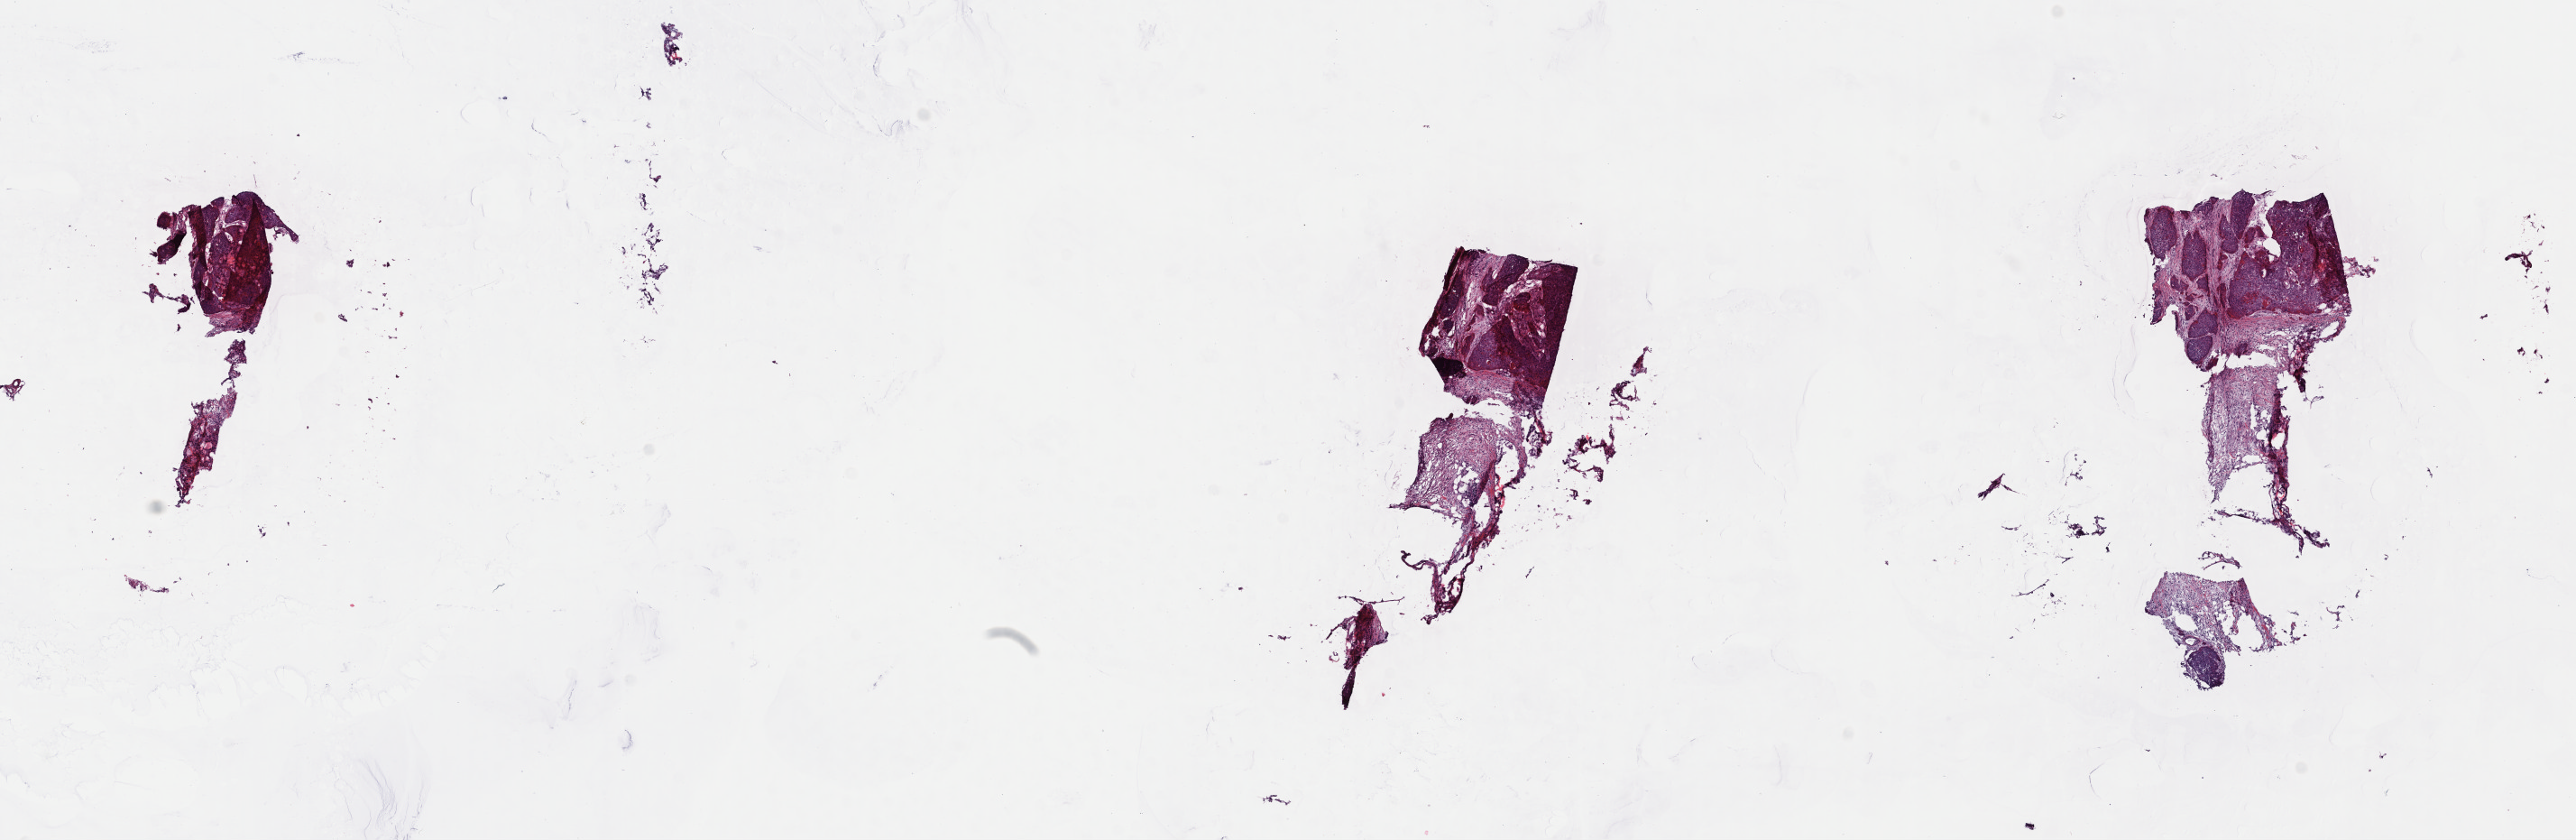
Whole-slide histology image, H&E — whole scanned area (about 22.4 x 7.3 mm, acquisition: 40x scan) shown as a low-resolution overview; frozen section from the top of the tissue portion; primary tumour sample from the cervix. Female patient; age at initial diagnosis 45 years. Histologic grade: G2 (moderately differentiated). Pathologist review of this section (percent, as recorded): tumour cells 60%, tumour nuclei 60%, normal cells 0%, stromal cells 30%, necrosis 10%. Inflammatory infiltration, as recorded: lymphocyte infiltration 40%, monocyte infiltration 20%, neutrophil infiltration 20%.
* diagnosis: Squamous cell carcinoma, large cell, nonkeratinizing, NOS (cervix uteri)
* FIGO stage: IVA